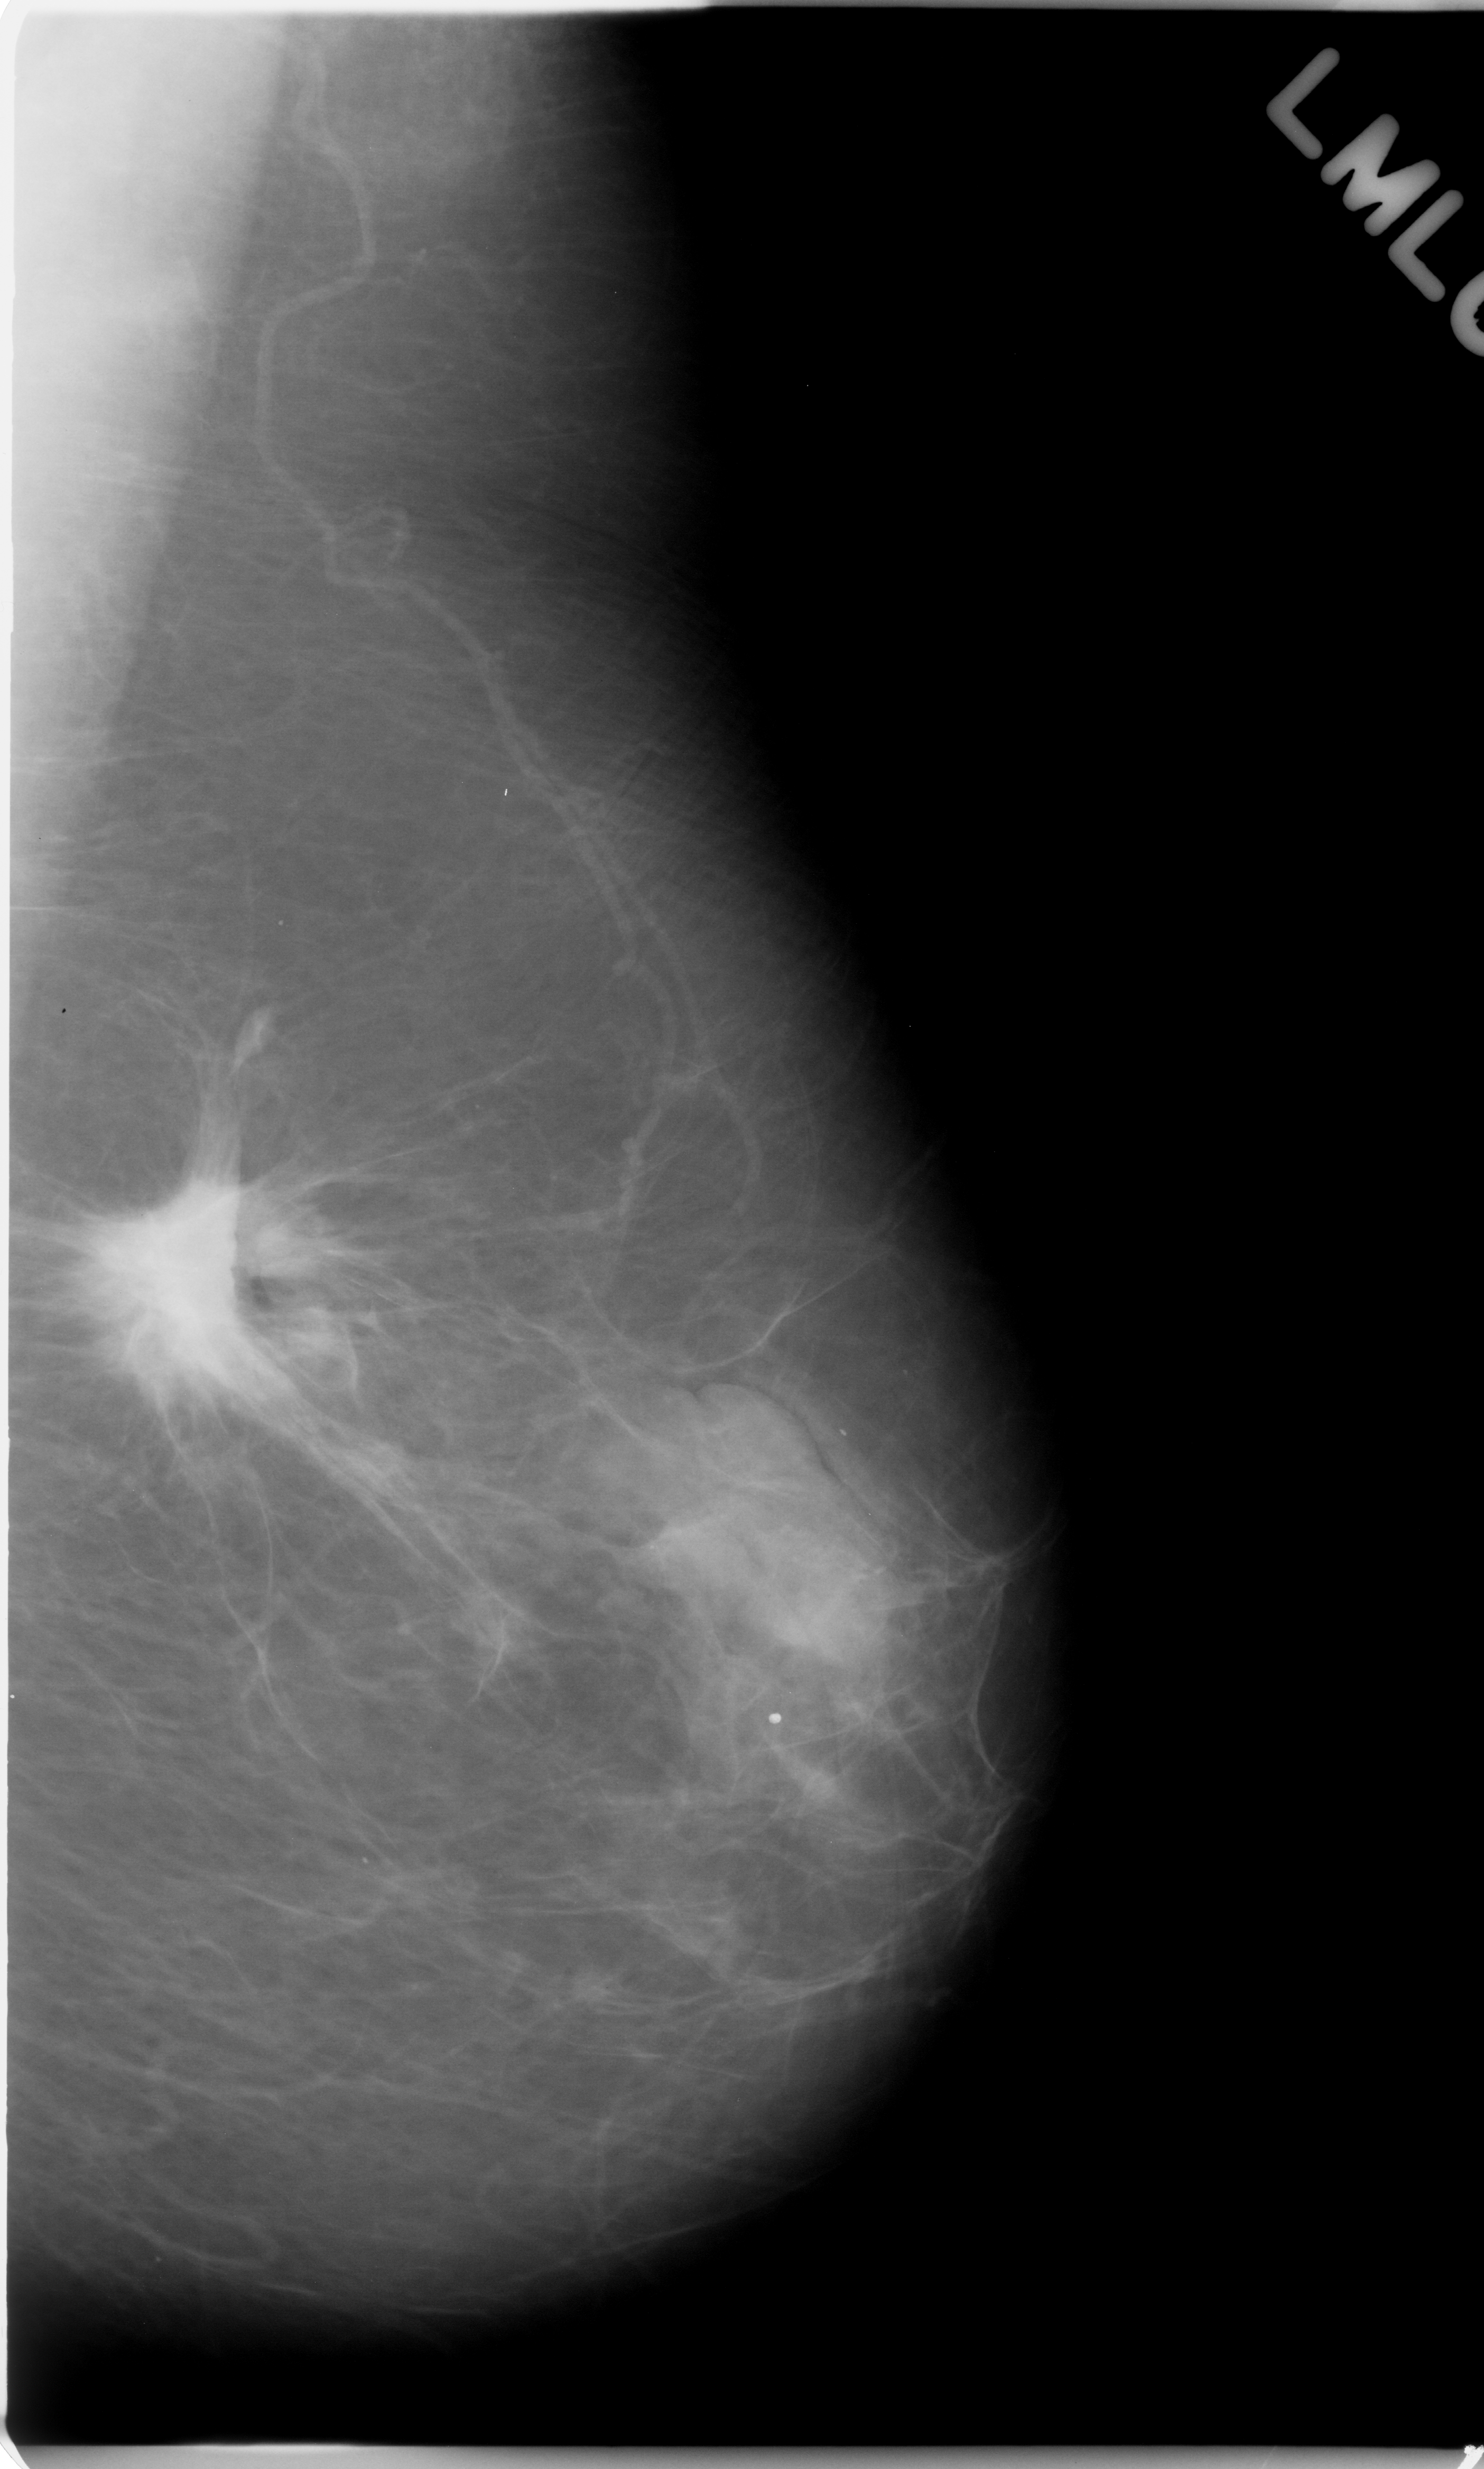
Digitized screen-film mammogram; left breast; mediolateral oblique (MLO) view; breast composition: almost entirely fatty (BI-RADS density category 1 of 4); 1484 × 2469 image matrix.
Expert-marked regions of interest on this image (one box per marked abnormality):
- mass, shape irregular, margins spiculated; BI-RADS assessment category 5; subtlety rating 5 on a 1 (subtle) to 5 (obvious) scale; pathology (as recorded): malignant: bounding box [x1, y1, x2, y2] px = [114, 1102, 390, 1452]